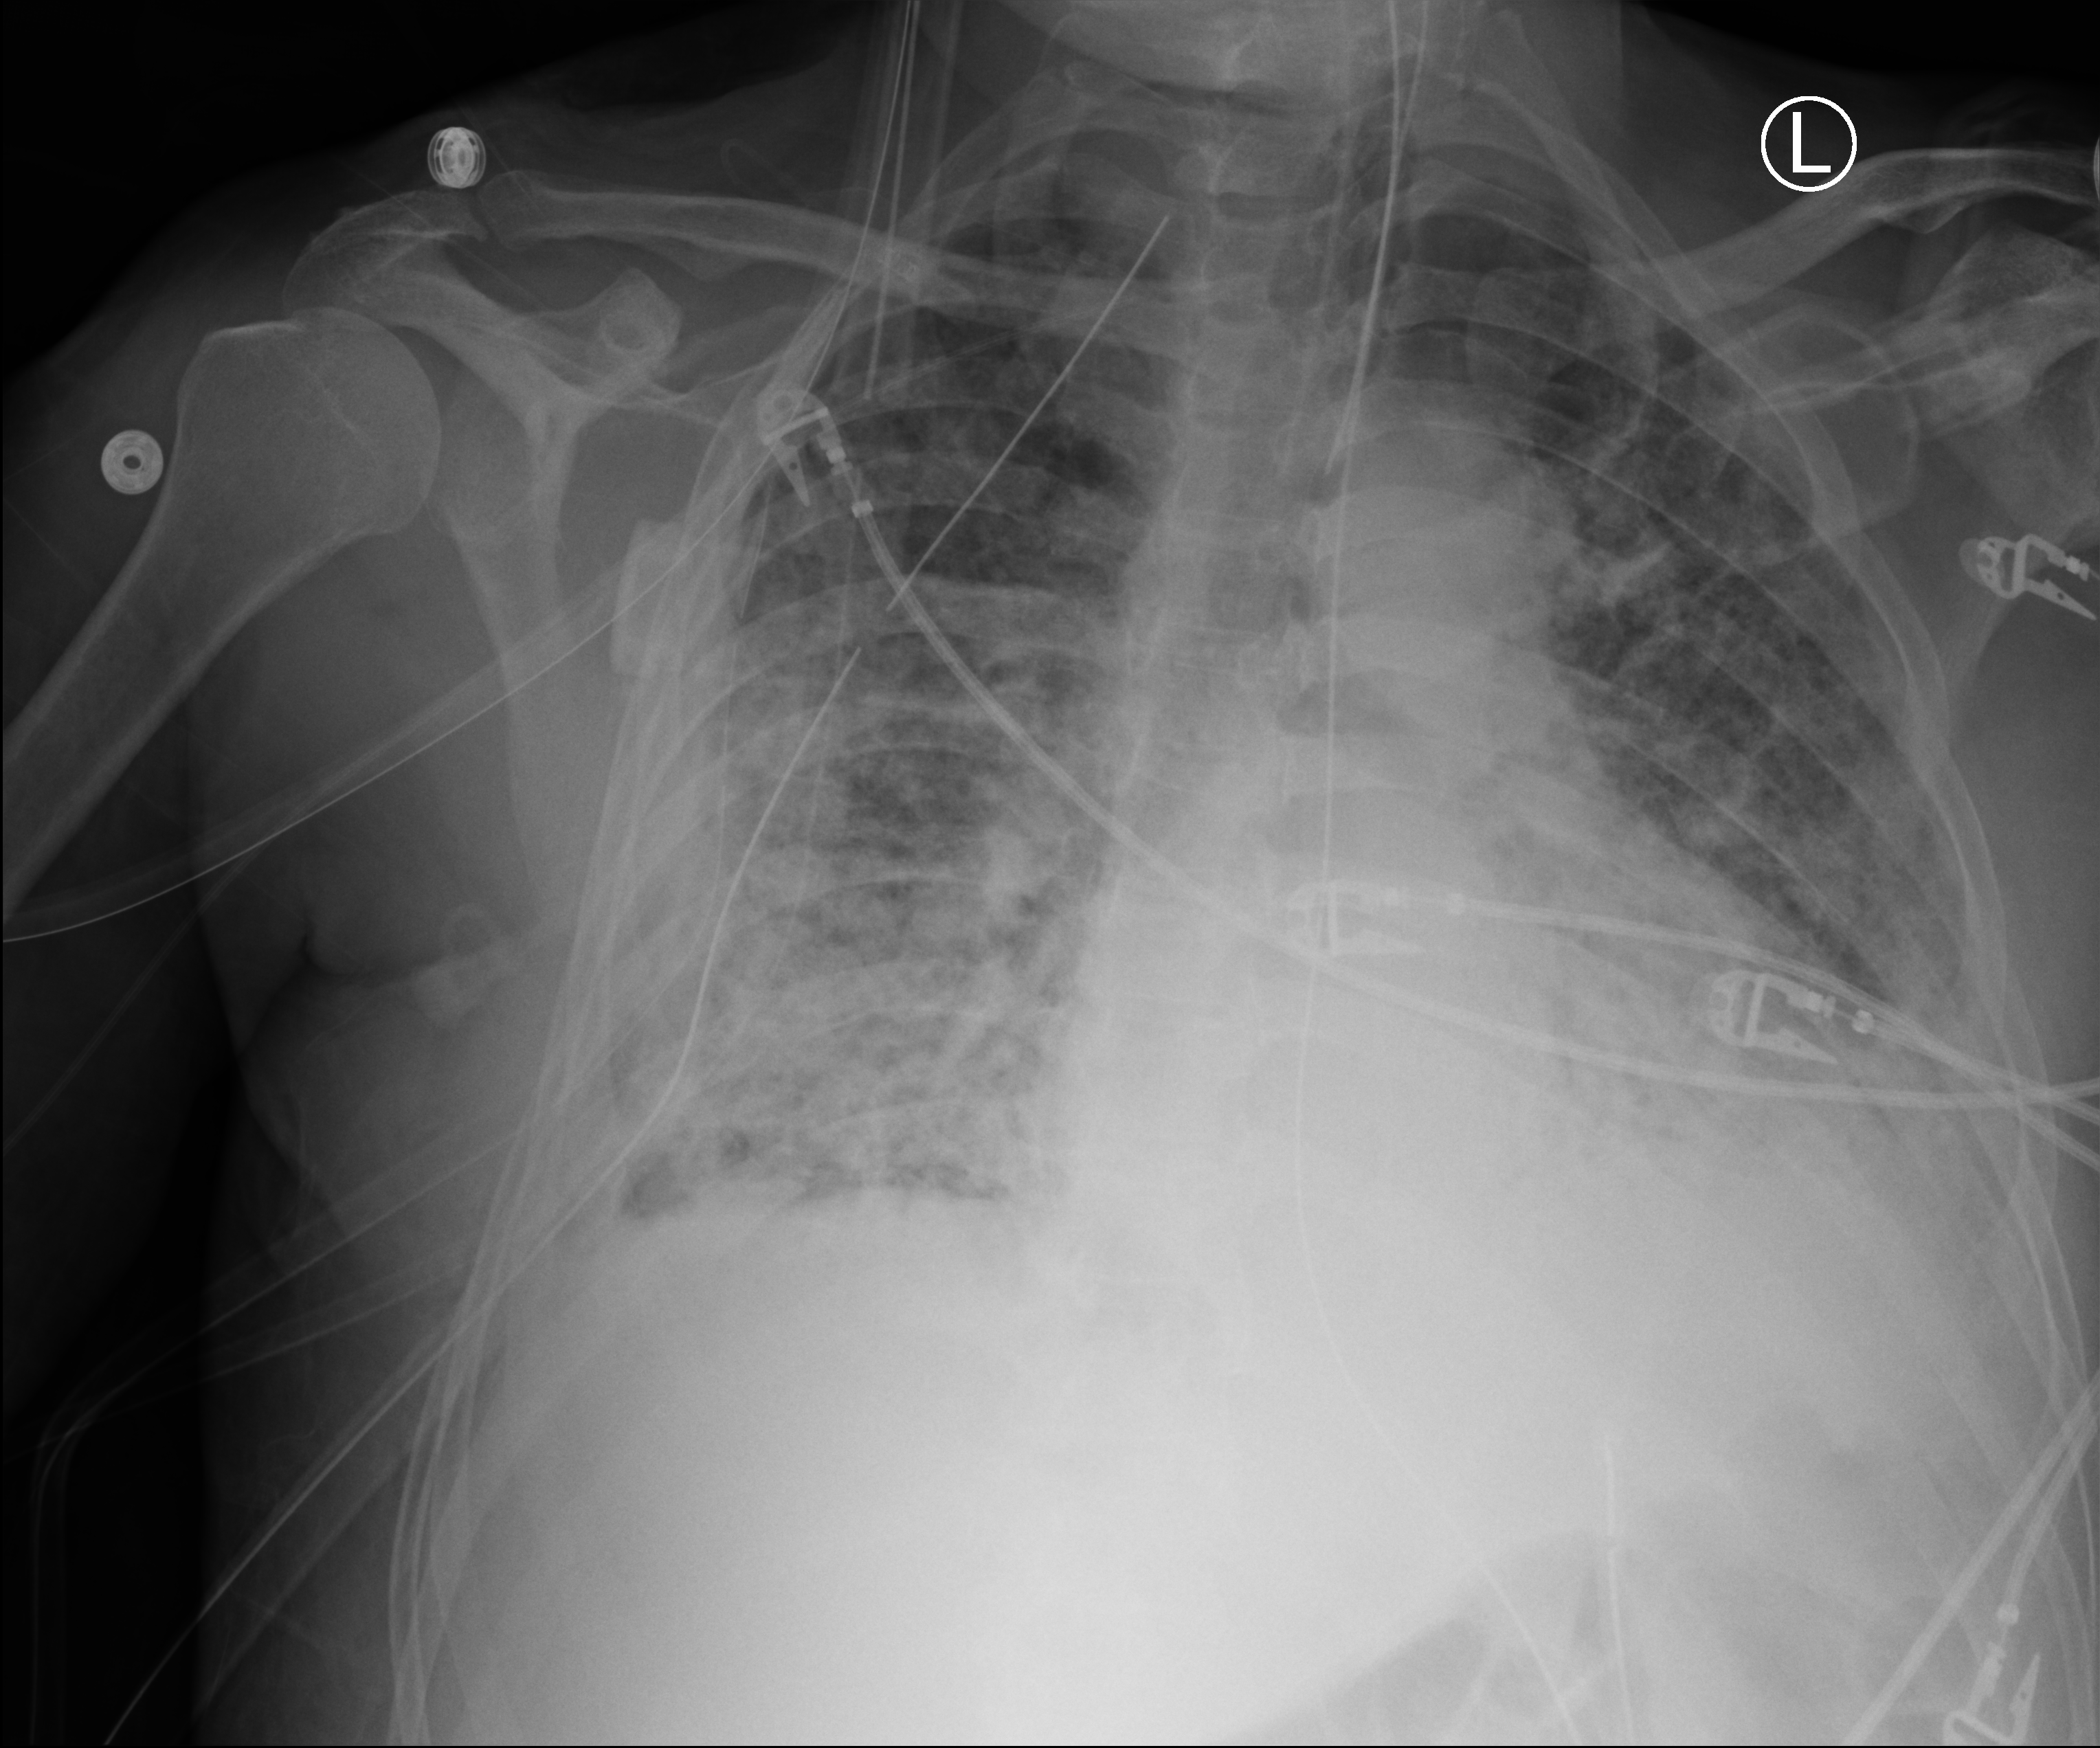
Bedside chest radiograph (computed radiography), anteroposterior (AP) projection. Patient hospitalised with COVID-19; male, aged 60–74 years.
From the hospital-stay record, not from the radiograph (when in the stay this image was taken is not recorded):
- mechanically ventilated during this hospital stay: yes